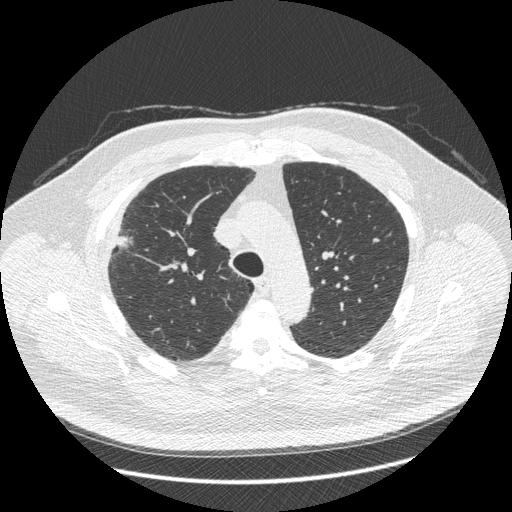
Chest CT (low-dose screening protocol), one axial image. Third screening round (two years after baseline). Lung window (W 1500 / L -600 HU). Standard (soft-tissue) reconstruction kernel (STANDARD). 120 kVp. Male participant, aged 66 years at enrolment. Current smoker at enrolment.
Expert-annotated lung lesion, bounding box [x1, y1, x2, y2] px = [88, 212, 148, 272]. Screening reader's record for this exam (one nodule recorded; not confirmed to be the boxed lesion): non-calcified nodule or mass ≥4 mm, right upper lobe, 48 × 25 mm, spiculated (stellate) margins, soft tissue attenuation, pre-existing on the prior screen: no. Official screen result: positive, other. Later outcome: lung cancer diagnosed 35 days after this screen — non-small cell carcinoma, right upper lobe, stage IV (AJCC 6th edition), 50 mm at pathology.